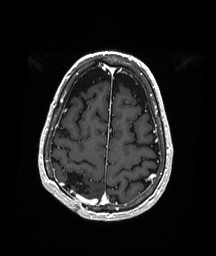
Brain MRI from a brain-tumour surgery series, one axial slice; position 57 of 192 along the scan axis; T1-weighted post-contrast; 216 × 256 image matrix, field of view 211 × 250 mm. Case-level facts recorded for this patient, not image findings: histopathology: Astrocytoma; WHO grade: 3; IDH mutation: yes.
Structures marked on this image (manually delineated by an expert):
- previous resection cavity: bounding box <62,171,90,197> (left, top, right, bottom; pixels)